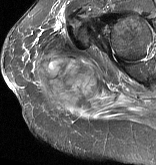
MRI of an extremity soft-tissue mass, one axial slice; STIR; MR volume resampled by the dataset authors to the PET/CT grid (not the native acquisition matrix); 3.27 mm slice thickness; 156 × 165 image matrix. Female patient. Case-level facts recorded for this patient, not image findings: histological type: epithelioid sarcoma with vascular differentiation; site of the primary tumour: right buttock.
Outlined on this slice (expert contour drawn on MRI and transferred to this co-registered scan by the dataset authors):
- gross tumour volume (mass): bounding box <35,55,100,106> (left, top, right, bottom; pixels)